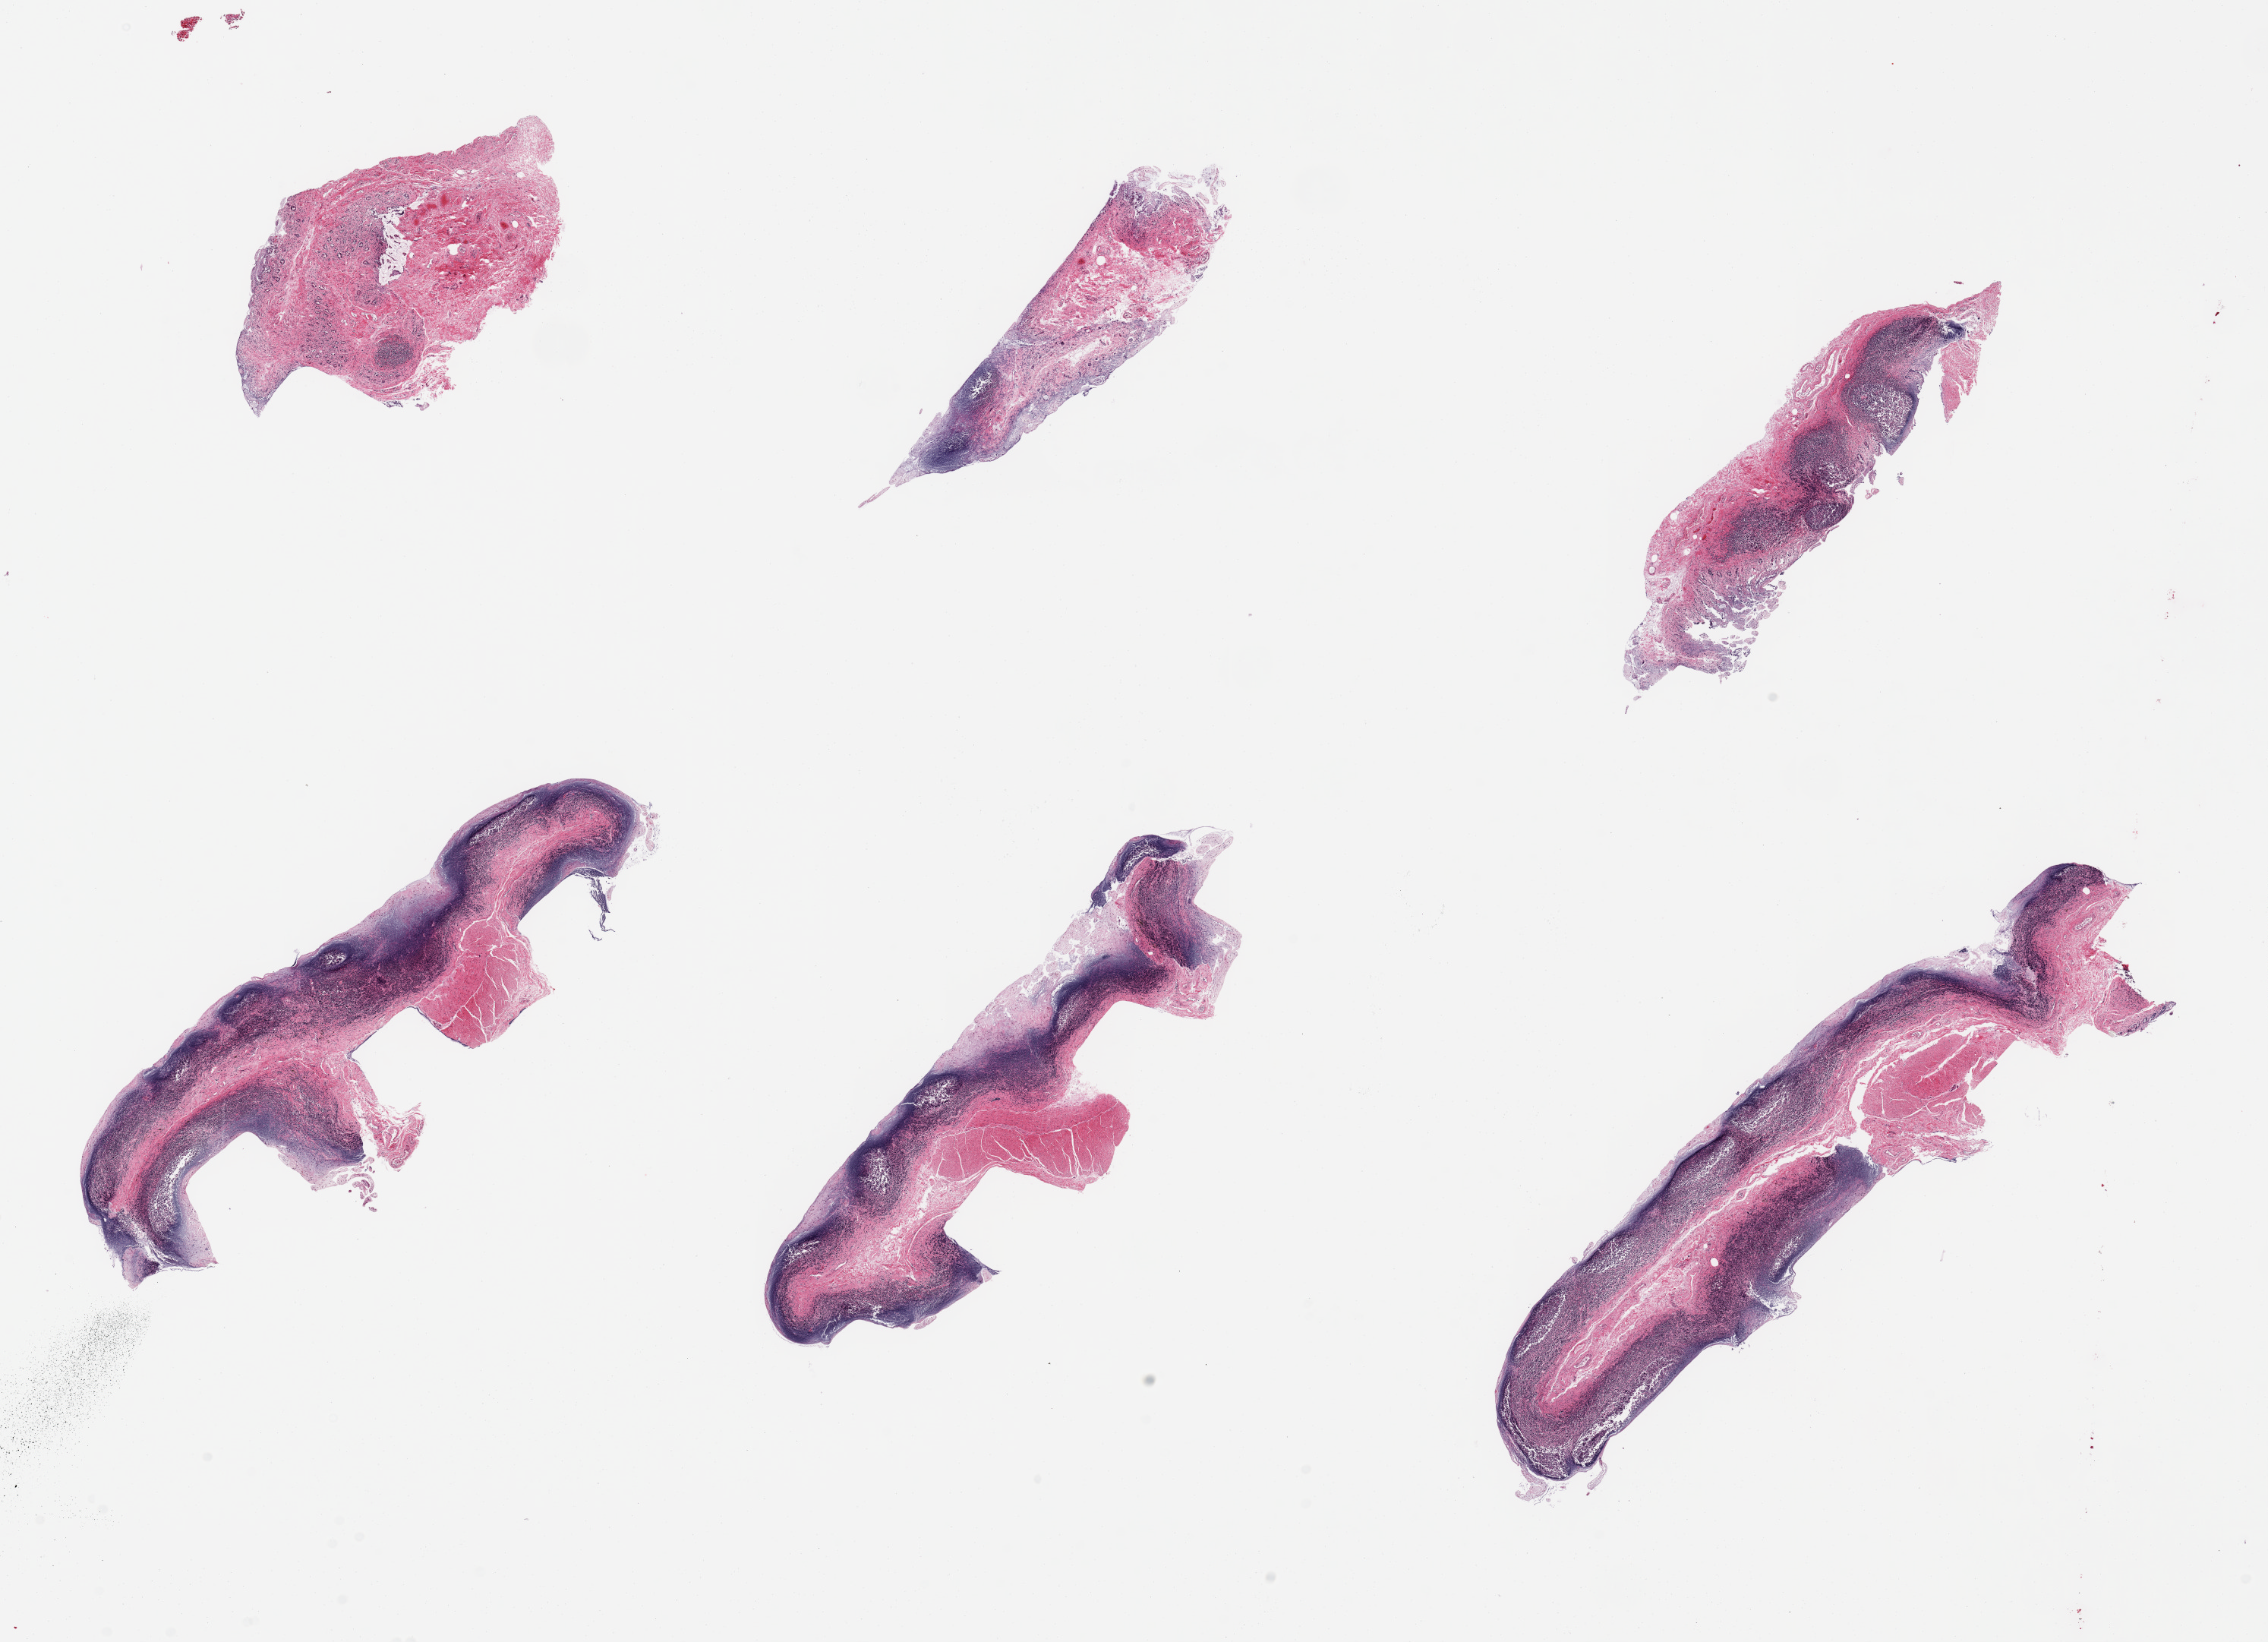
Digitized hematoxylin and eosin (H&E)-stained section — a low-resolution overview of the entire scanned area, about 23.6 x 17.1 mm. PAXgene-fixed, paraffin-embedded tissue. Sampled site (target tissue): ileum. Tissue donor sample. Donor sex: male.
Pathologist's review note for this sample: 6 pieces, advanced autolysis; target lymphoid aggregates are ~40% of tissue.